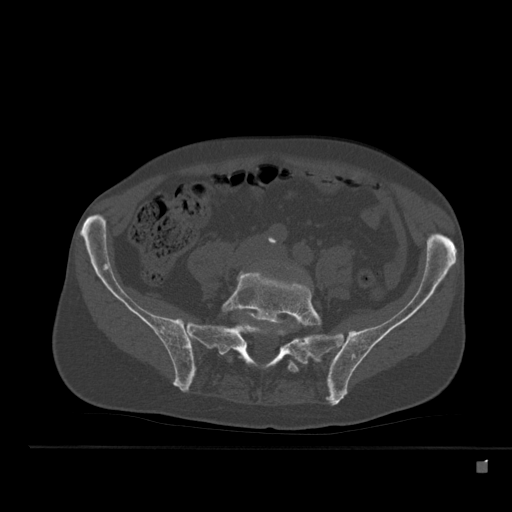
CT including the spine, one axial slice; position 120 of 517 along the scan axis; reconstruction kernel Br40s; 120 kVp; bone window (W 1800 / L 400 HU); 1.5 mm slice thickness; 512 × 512 image matrix, field of view 408 × 408 mm. Male patient, age 70 years. Case-level facts recorded for this patient, not image findings: primary cancer: renal; vertebrae with lytic lesions (as recorded): T4, T6, T10, T12, L3, L4, L5.
Outlined on this slice (semi-automatically segmented with operator editing):
- L5 vertebra: box from (x=221, y=272) to (x=323, y=373) px